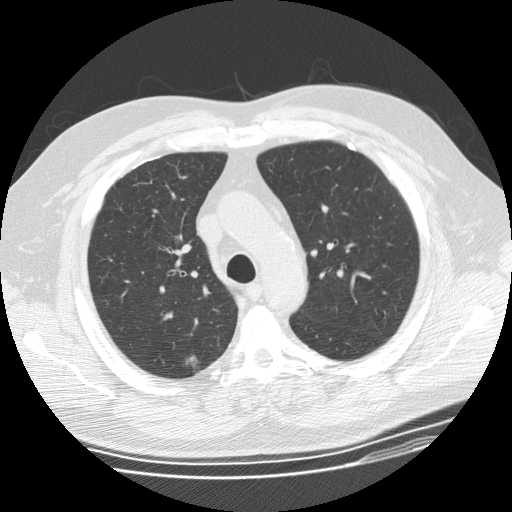
Low-dose screening chest CT, one axial slice; slice 110 of 155 in the series (ordered by position); reconstruction kernel STANDARD; lung window (W 1500 / L -600 HU); 512 × 512 image matrix, field of view 380 × 380 mm.
Structures marked on this image (outlined manually by an expert reader):
- lesion 1 (tumor, upper lobe of right lung): bounding box <185,355,203,374> (left, top, right, bottom; pixels)